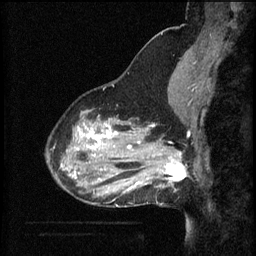
Breast MRI (dynamic contrast-enhanced), one sagittal slice. Slice 19 of 60 in the series (ordered by position). 3 images stored at this slice position (order not interpretable as contrast timing). 1.5 T. TE 4.2 ms, TR 8.2 ms. 2 mm slice thickness. 256 × 256 image matrix, field of view 200 × 200 mm. Patient: female, 37 years.
Outlined on this slice (semi-automatic segmentation, software-assisted and operator-edited):
- analysis volume of interest (the breast-tissue region the enhancement analysis was run in; not a lesion): bounding box [x1, y1, x2, y2] px = [148, 140, 191, 187]
- tumour enhancement mask (voxels above the 70 % enhancement threshold inside the analysis volume of interest): [148, 152, 187, 183]